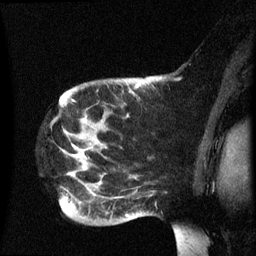
Breast MRI (dynamic contrast-enhanced), one sagittal slice. Position 50 of 60 along the scan axis. Dynamic contrast-enhanced series, image 2 of 3 at this slice position (ordered by acquisition). 1.5 T. TE 4.2 ms, TR 8.4 ms. 2.5 mm slice thickness. 256 × 256 image matrix. Female patient, age 49 years.
Annotated regions visible in this slice (semi-automatically segmented with operator editing):
- analysis volume of interest (the breast-tissue region the enhancement analysis was run in; not a lesion): bounding box <60,76,185,235> (left, top, right, bottom; pixels)
- tumour enhancement mask (voxels above the 70 % enhancement threshold inside the analysis volume of interest): <127,84,140,217>